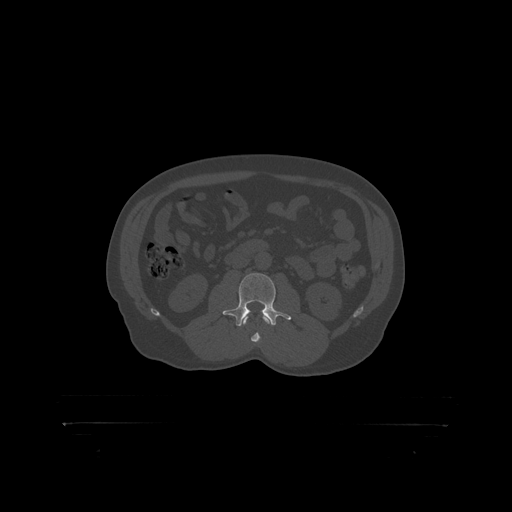
CT including the spine, one axial slice; position 274 of 399 along the scan axis; 120 kVp; bone window (W 1800 / L 400 HU); 512 × 512 image matrix. Male patient, age 46 years. From the clinical record (not read from this slice): primary cancer: skin.
Annotated regions visible in this slice (semi-automatic segmentation, software-assisted and operator-edited):
- L2 vertebra: bounding box <244,315,249,319> (left, top, right, bottom; pixels)
- L3 vertebra: <226,273,282,319>